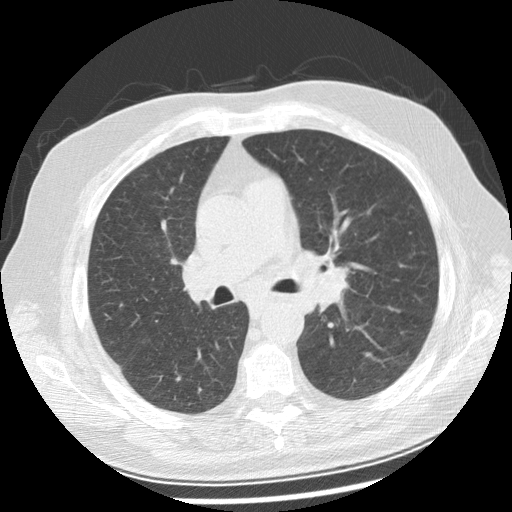
Chest CT (low-dose screening protocol), one axial image; baseline annual screen; lung window (W 1500 / L -600 HU); 2.5 mm slice thickness; 512 × 512 image matrix. Male, age 70 years at enrolment. Current smoker at enrolment.
Expert-annotated lung lesion, bounding box (x1, y1, x2, y2) in pixels: (281, 242, 363, 309). No non-calcified nodule or mass ≥4 mm was recorded by the screening reader at this exam.